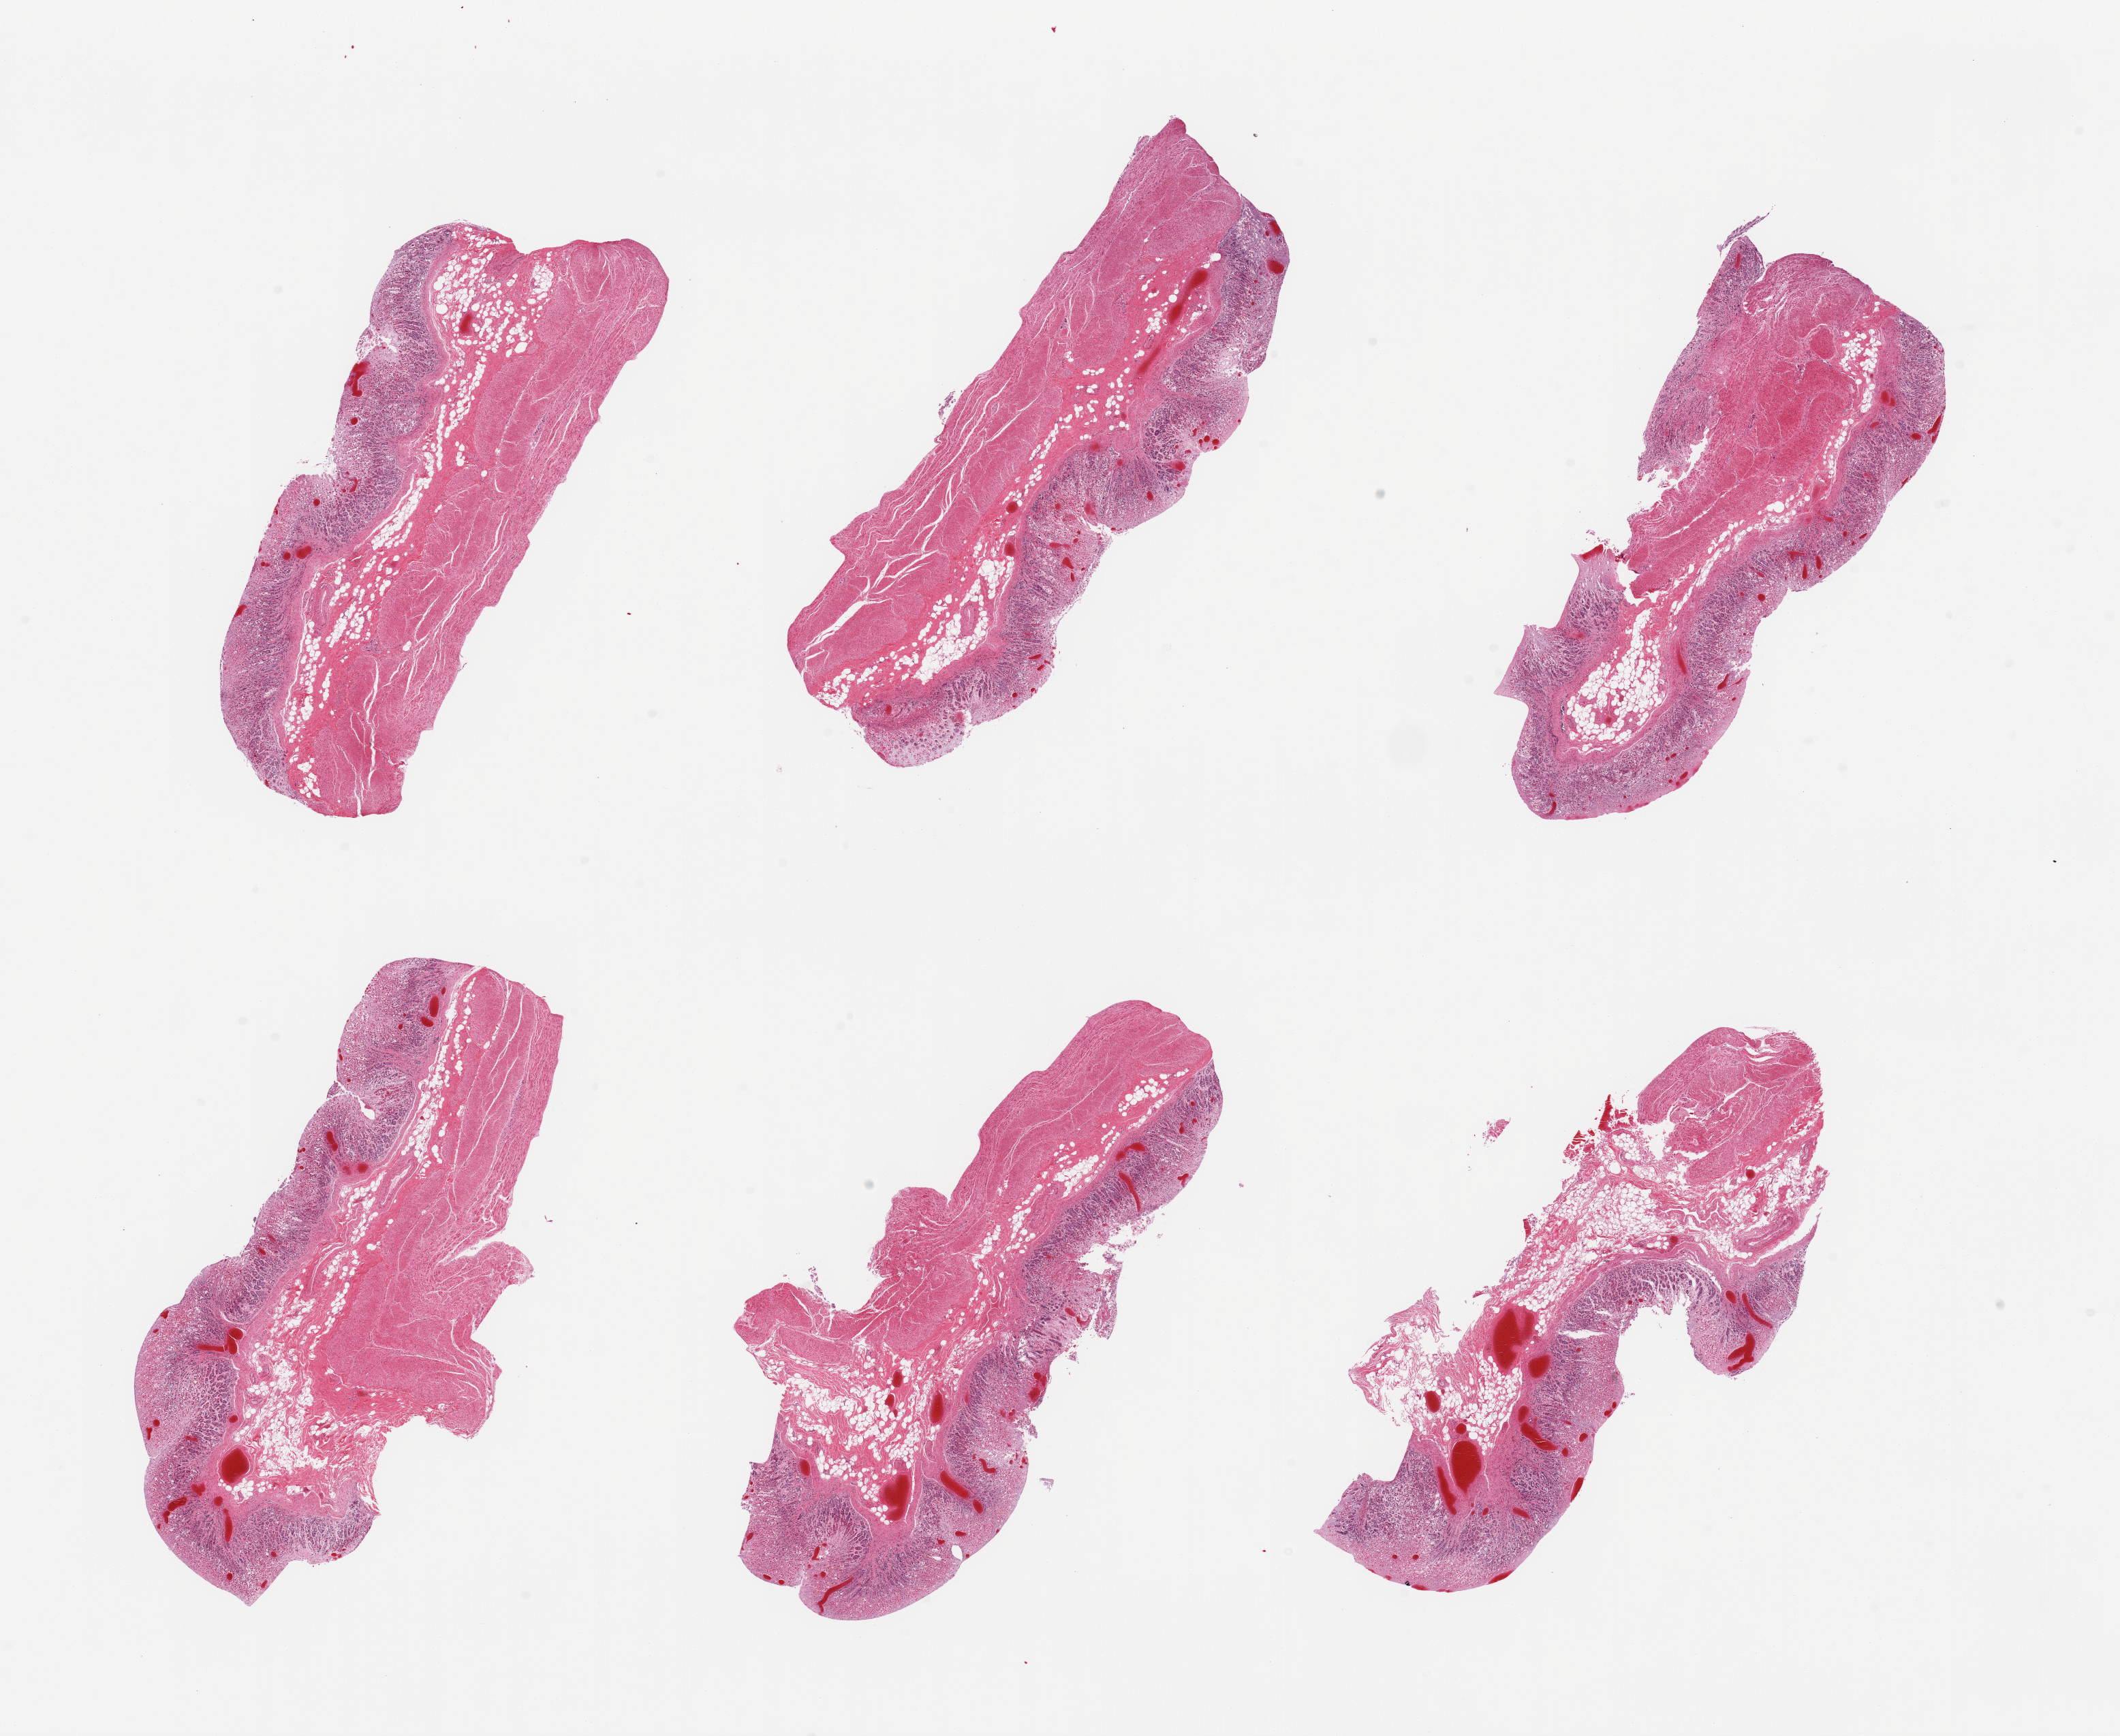
Haematoxylin and eosin whole-slide image — low-resolution overview of the scanned area, about 24.6 x 20.2 mm (slide scanned at 20x); PAXgene-fixed, paraffin-embedded tissue; sampled site (target tissue): stomach; donor tissue sample. Donor sex: male.
Pathologist's review note for this sample: 6 pieces; mucosa severely autolyzed; muscle moderately autolyzed.